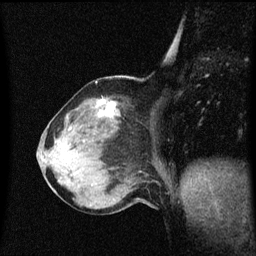
Breast MRI (dynamic contrast-enhanced), one sagittal slice. Dynamic contrast-enhanced series, image 2 of 3 at this slice position (ordered by acquisition). 1.5 T. TE 4.2 ms, TR 8.4 ms. 256 × 256 image matrix, field of view 200 × 200 mm. Female patient, age 64 years. Case-level facts recorded for this patient, not image findings: setting: breast cancer imaged before/during neoadjuvant chemotherapy; receptor status: HR-positive, HER2-negative.
Annotated regions visible in this slice (semi-automatic segmentation, software-assisted and operator-edited):
- analysis volume of interest (the breast-tissue region the enhancement analysis was run in; not a lesion): box from (x=58, y=98) to (x=123, y=167) px
- tumour enhancement mask (voxels above the 70 % enhancement threshold inside the analysis volume of interest): (x=98, y=100)–(x=115, y=117)